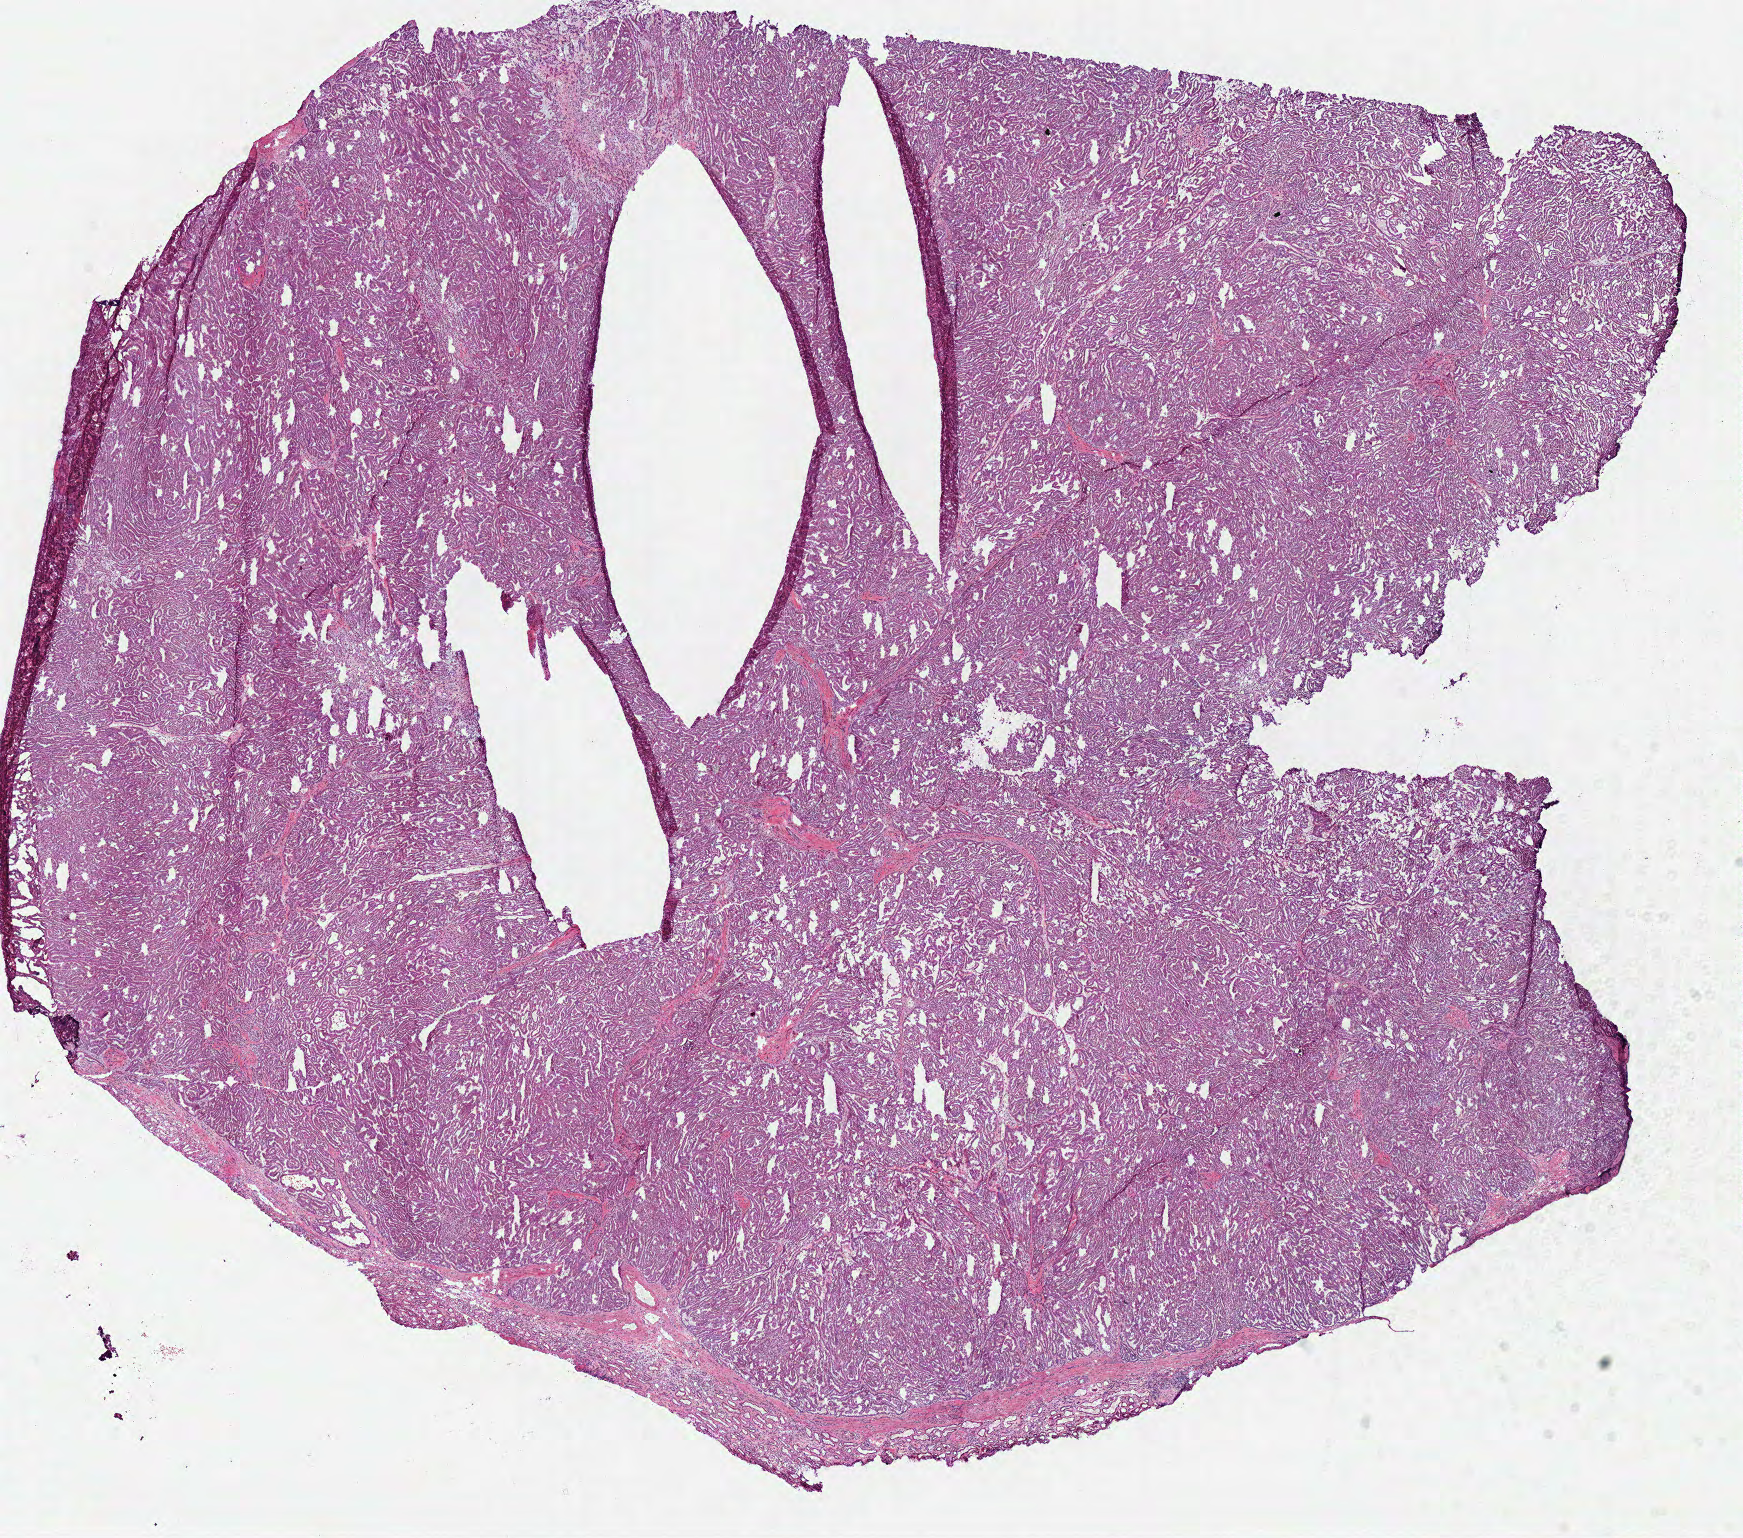
Digitized H&E tissue section (whole slide), whole scanned area (about 13.7 x 12.1 mm) shown as a low-resolution overview. Frozen section from the bottom of the tissue portion. Primary tumour sample from the kidney. Patient: male, age at initial diagnosis 46 years.
Histologic diagnosis: Papillary adenocarcinoma, NOS.